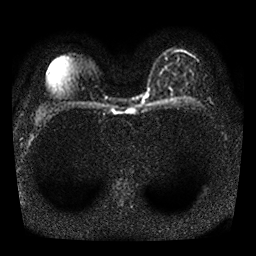
Breast MRI, one axial slice. Diffusion-weighted series; image 2 of 4 stored at this slice position (different b-values; order by instance number). 1.5 T. 256 × 256 image matrix, field of view 310 × 310 mm. Female patient.
Annotated regions visible in this slice (expert manual segmentation):
- tumour on diffusion-weighted imaging: box from (x=170, y=88) to (x=173, y=92) px